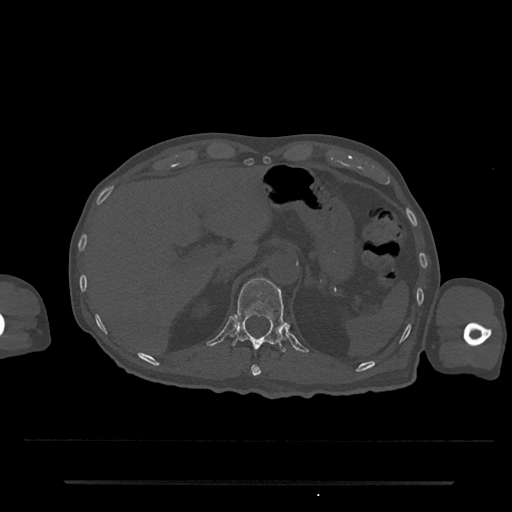
CT including the spine, one axial slice. Position 199 of 797 along the scan axis. Reconstruction kernel Br40s/3. 120 kVp. Bone window (W 1800 / L 400 HU). 0.5 mm slice thickness. 512 × 512 image matrix. Male patient, age 74 years. Case-level facts recorded for this patient, not image findings: primary cancer: prostate.
Outlined on this slice (semi-automatic segmentation, software-assisted and operator-edited):
- T11 vertebra: bounding box (x1, y1, x2, y2) in pixels: (251, 365, 261, 377)
- T12 vertebra: (230, 278, 287, 352)